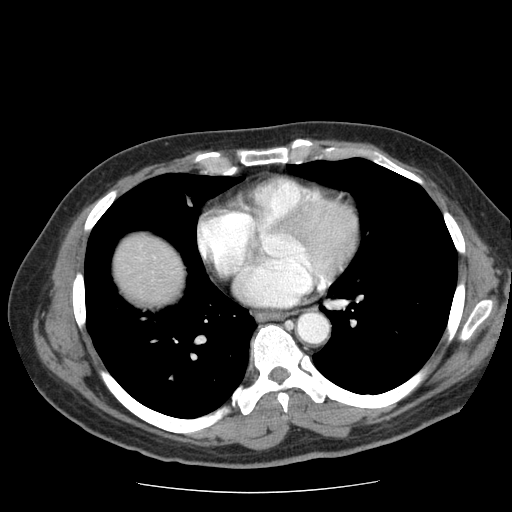
Contrast-enhanced abdominal CT (liver protocol), one axial slice. Reconstruction kernel STANDARD. 120 kVp. Soft-tissue window (W 400 / L 40 HU). 2.5 mm slice thickness. 512 × 512 image matrix, field of view 360 × 360 mm. From the clinical record (not read from this slice): diagnosis: hepatocellular carcinoma (patient treated with transarterial chemoembolisation; whether this scan precedes or follows treatment is not stated here); TNM stage (as recorded): Stage-IIIA; Child-Pugh class: A; tumour nodularity: multinodular.
Annotated regions visible in this slice (semi-automatically segmented with operator editing):
- liver parenchyma outside the tumour (the mass and vessels are separate outlines, so this box may not span the whole liver): bounding box (x1, y1, x2, y2) in pixels: (114, 234, 184, 304)